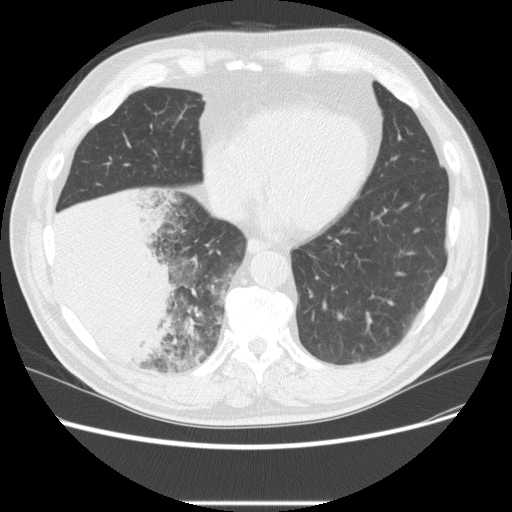
Low-dose screening chest CT, one axial slice. Slice 71 of 233 in the series (ordered by position). 120 kVp. Lung window (W 1500 / L -600 HU). 512 × 512 image matrix, field of view 380 × 380 mm.
Outlined on this slice (manually delineated by an expert):
- lesion 3 (tumor, lower lobe of right lung): box from (x=52, y=188) to (x=178, y=368) px